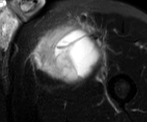
MRI of an extremity soft-tissue mass, one axial slice; position 45 of 52 along the scan axis; T2-weighted fat-saturated; MR volume resampled by the dataset authors to the PET/CT grid (not the native acquisition matrix); 3.27 mm slice thickness; 147 × 122 image matrix. Male patient. From the clinical record (not read from this slice): histological type: pleiomorphic liposarcoma; grade: high; site of the primary tumour: left thigh.
Structures marked on this image (expert contour drawn on MRI and transferred to this co-registered scan by the dataset authors):
- gross tumour volume including surrounding oedema: box from (x=37, y=23) to (x=104, y=77) px
- gross tumour volume (mass): (x=37, y=30)–(x=92, y=76)